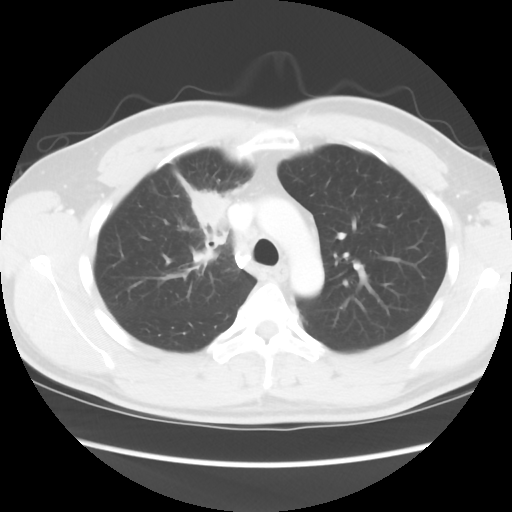
Chest CT, one axial slice. Reconstruction kernel STANDARD. 120 kVp. Lung window (W 1500 / L -600 HU). 5 mm slice thickness. 512 × 512 image matrix. Patient: male, 35 years. From the clinical record (not read from this slice): clinical TNM (as recorded): T1c N1 M1b.
Annotated regions visible in this slice (bounding box drawn by a radiologist):
- lung tumour (recorded histology: adenocarcinoma): bounding box (x1, y1, x2, y2) in pixels: (179, 186, 230, 233)